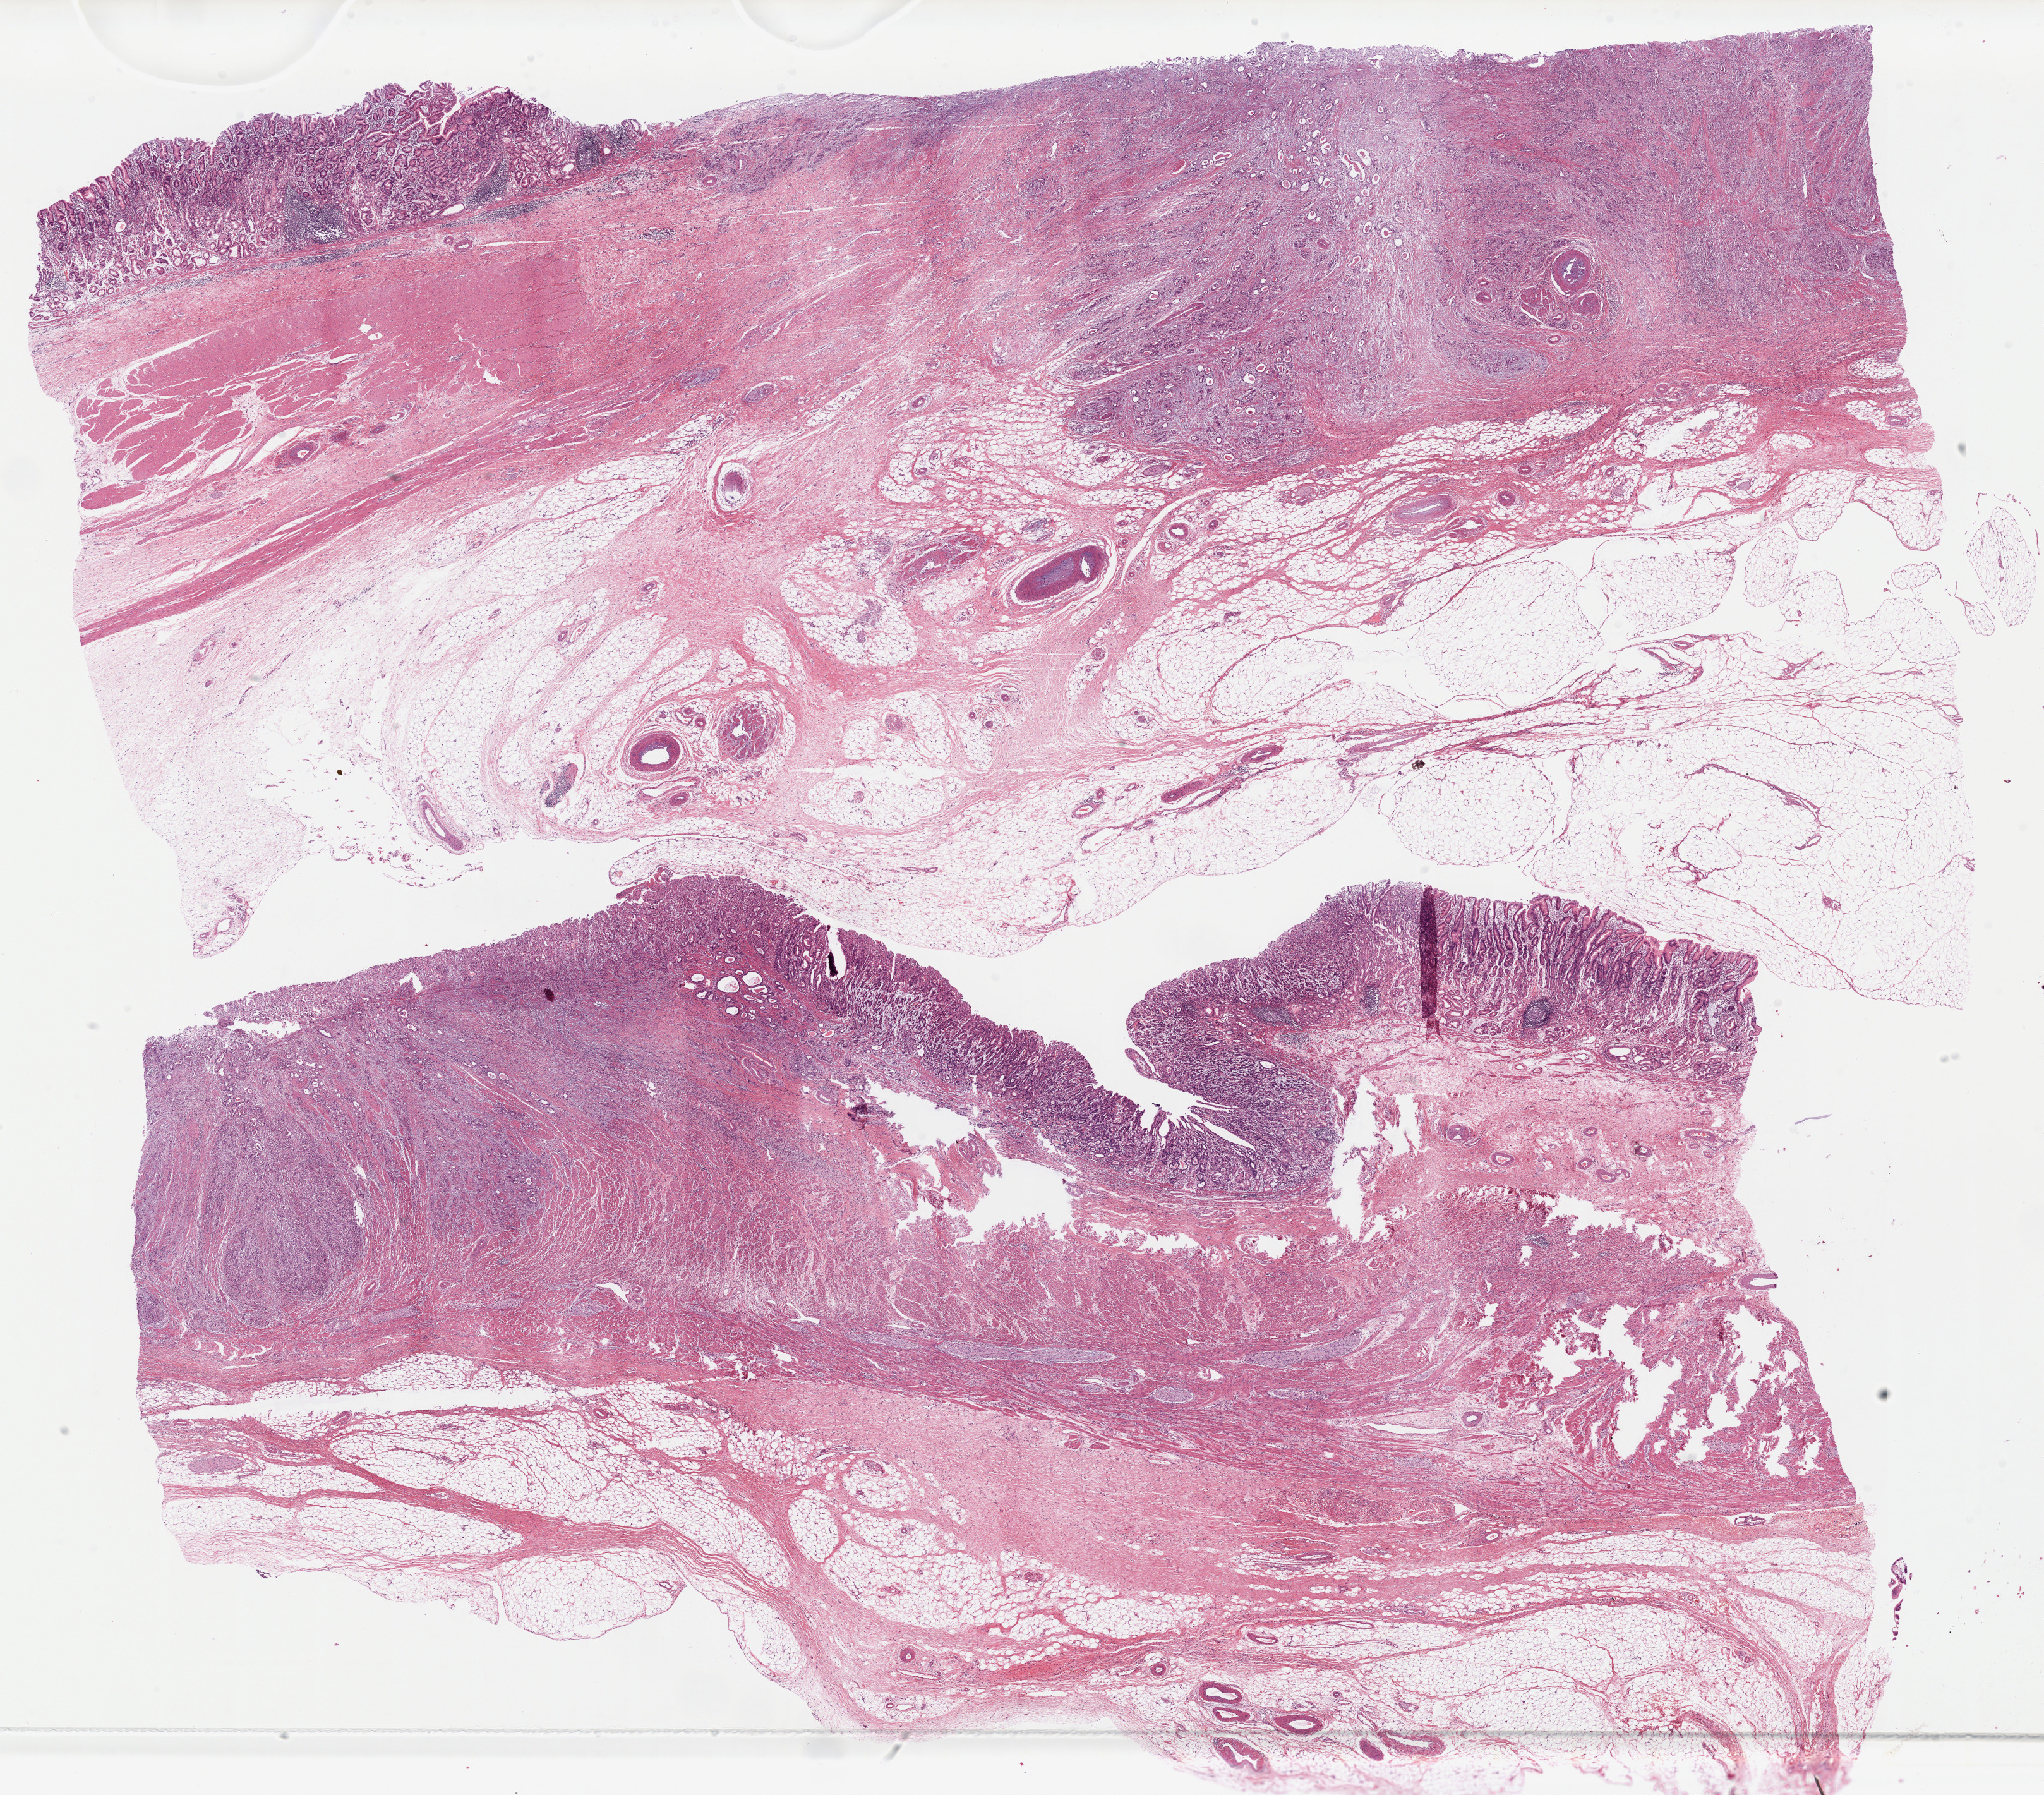
Digitized H&E-stained tissue section (whole slide), a low-resolution overview of the entire scanned area, about 25.6 x 22.5 mm (from a 20x scan). FFPE section. Sample: primary tumour, stomach. Patient: female, age at initial diagnosis 72 years. Histologic grade: G2 (moderately differentiated).
- TNM: T3 N2 M0
- AJCC pathologic stage: IIIA (7th edition)
- pathologic diagnosis: Tubular adenocarcinoma